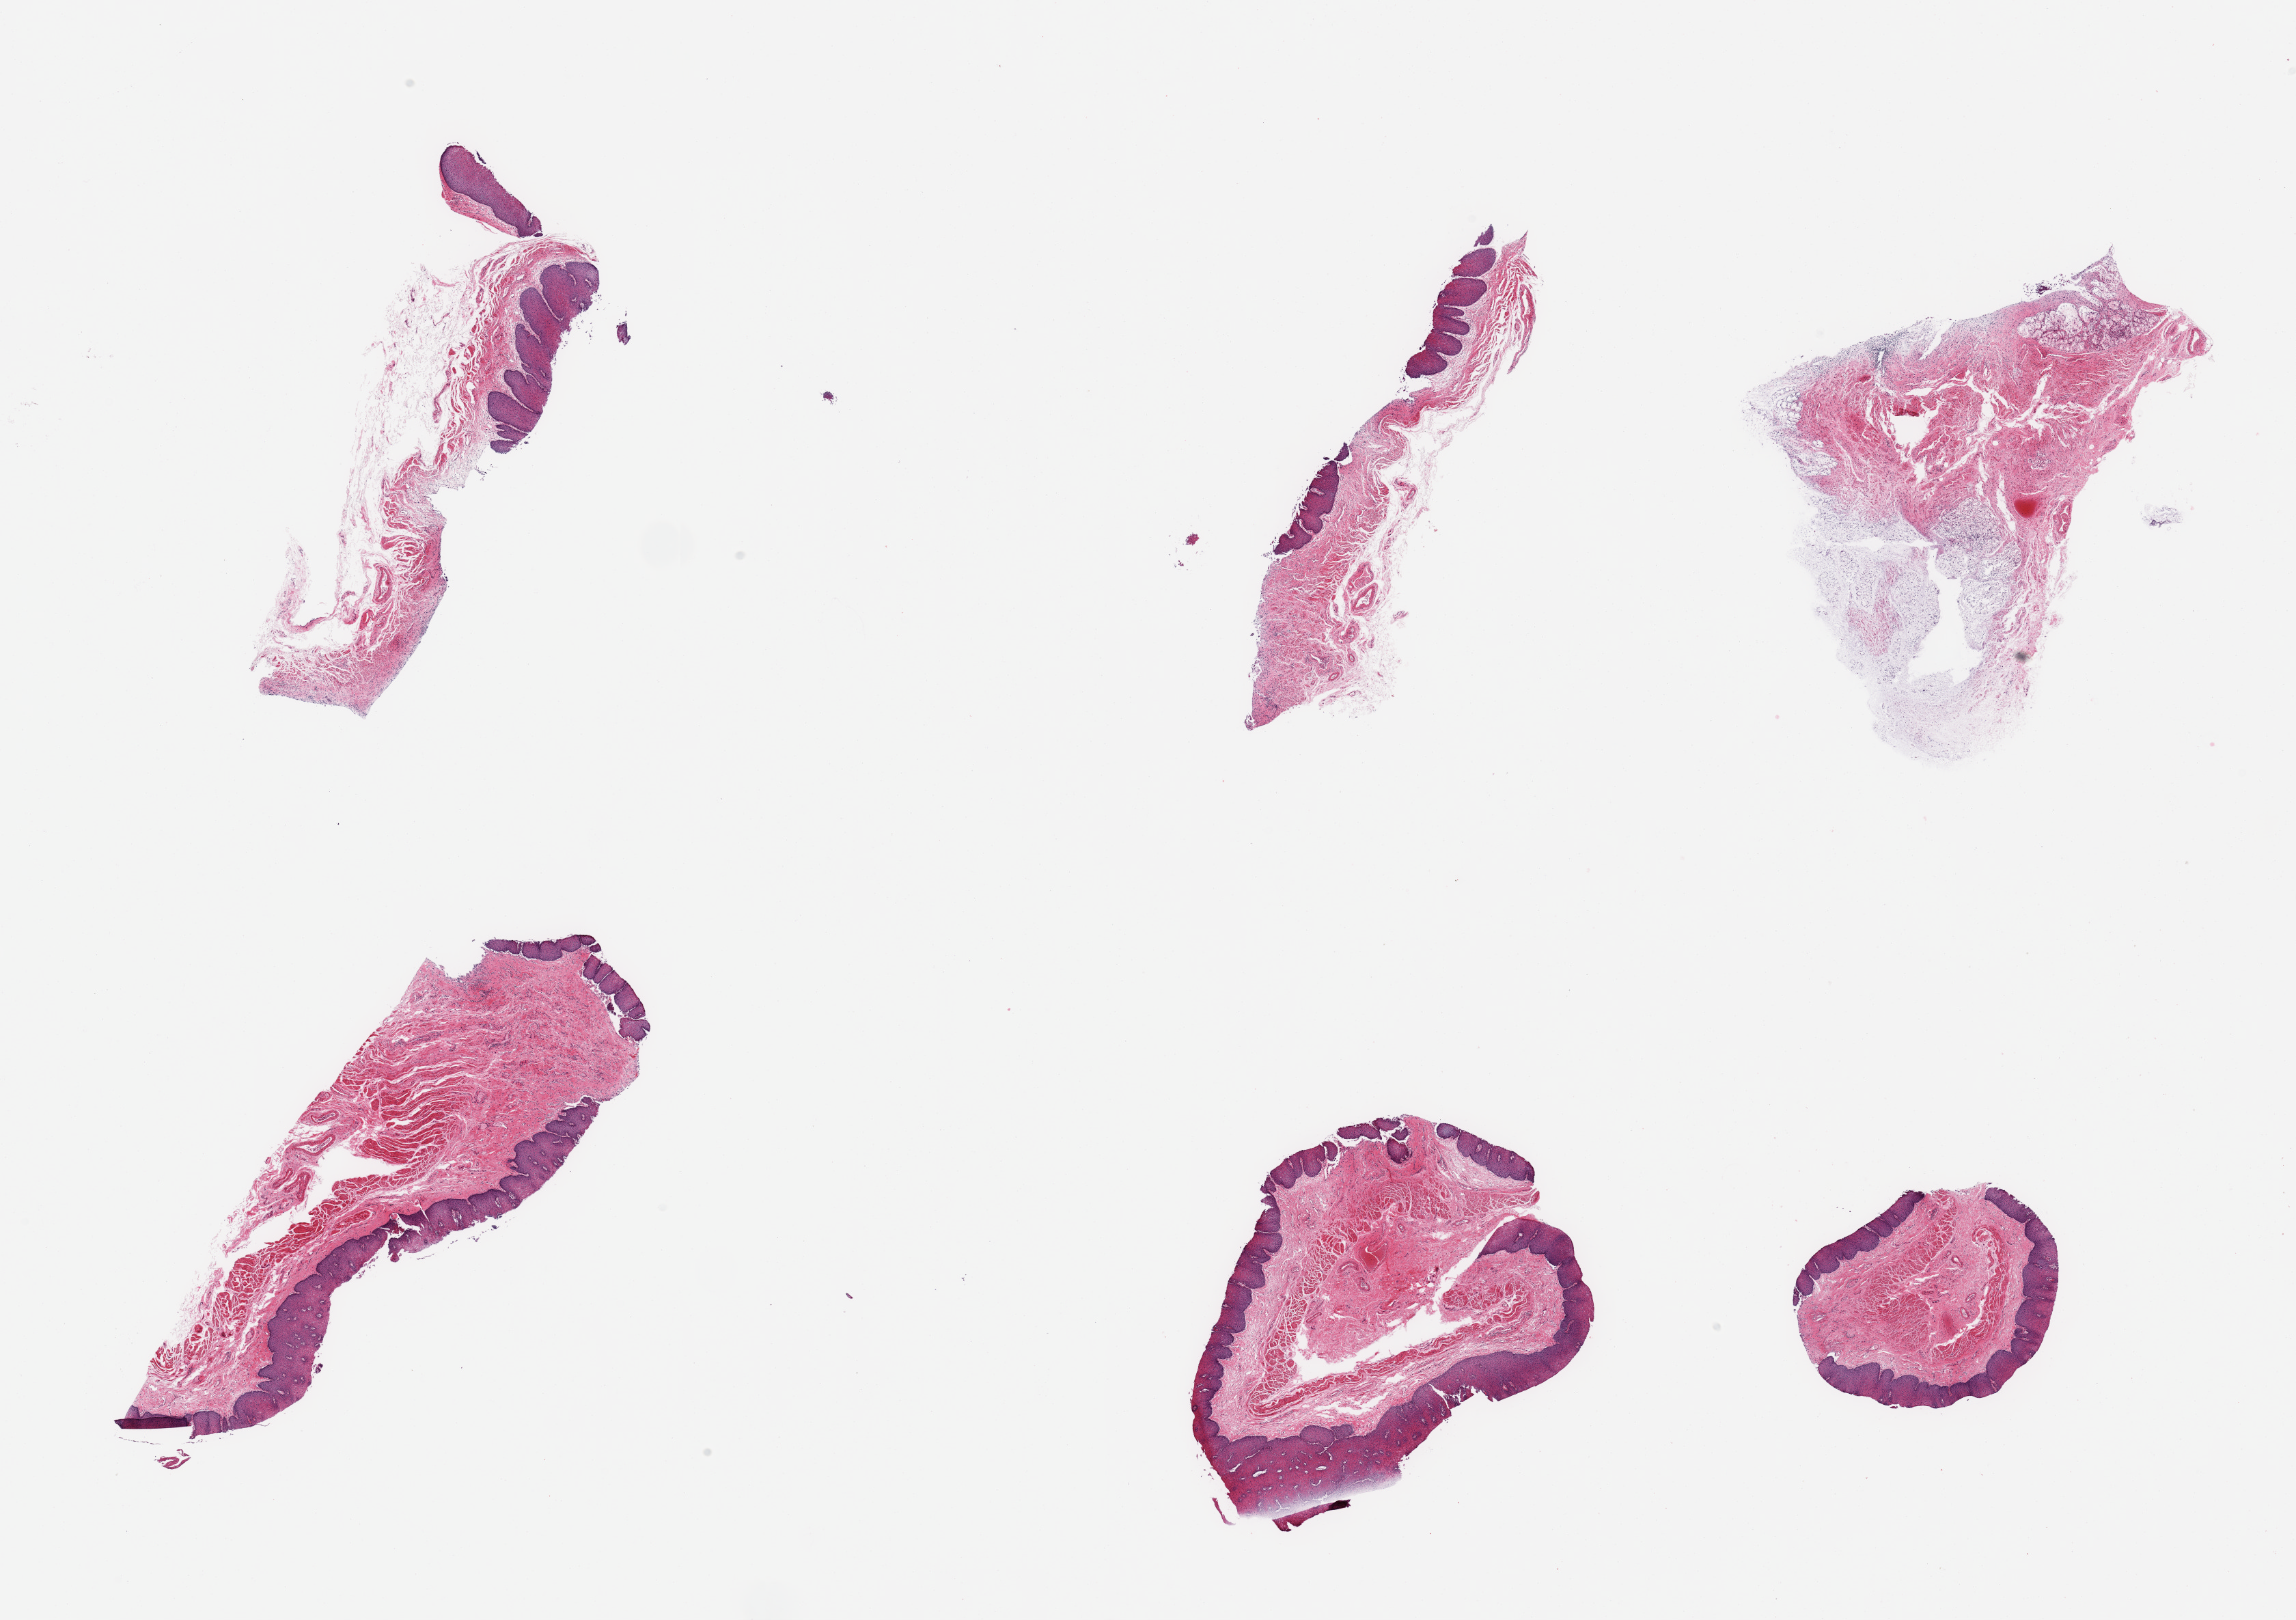
Hematoxylin and eosin (H&E) whole-slide image, whole scanned area (about 26.6 x 18.8 mm) shown as a low-resolution overview; PAXgene-fixed, paraffin-embedded tissue; section of esophageal mucous membrane (target tissue); donor tissue sample. Donor sex: female.
• reviewer comment on this tissue sample: 6 pieces; mucosa is entirely sloughed on 1 piece which predominantly consists of autolyzed submucosal glands